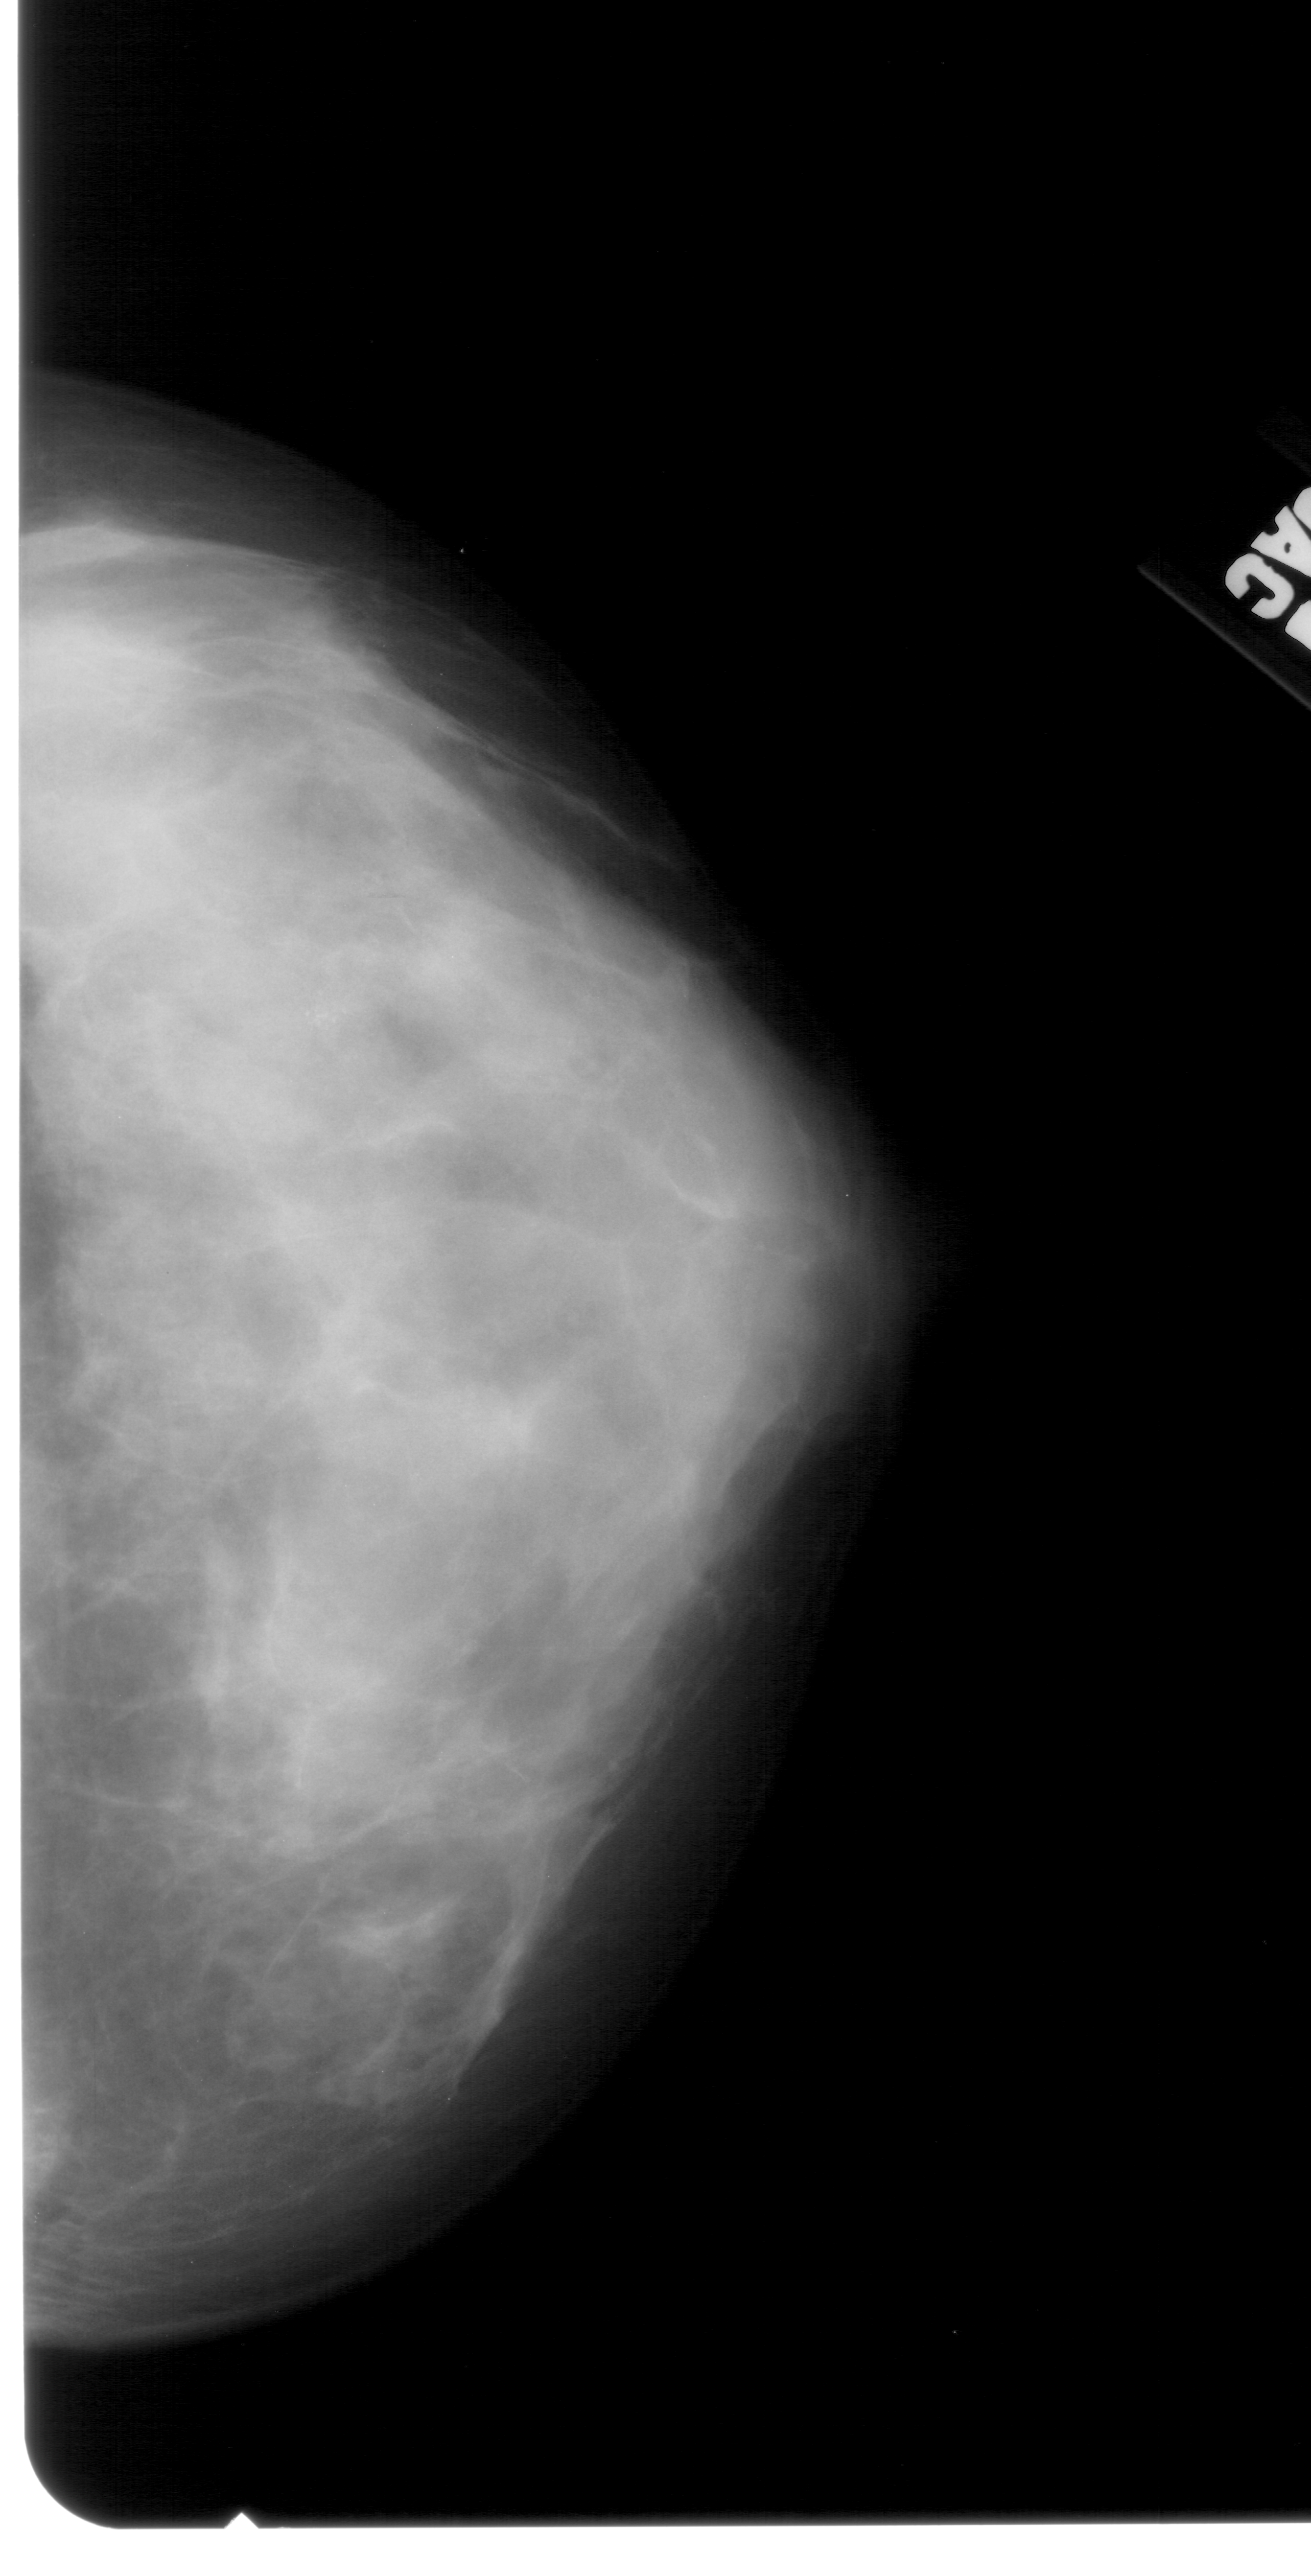
Mammogram (digitized film); right breast; craniocaudal (CC) view.
Finding: calcifications, morphology pleomorphic, distribution clustered; BI-RADS assessment category 4; subtlety rating 4 on a 1 (subtle) to 5 (obvious) scale; pathology (as recorded): benign.